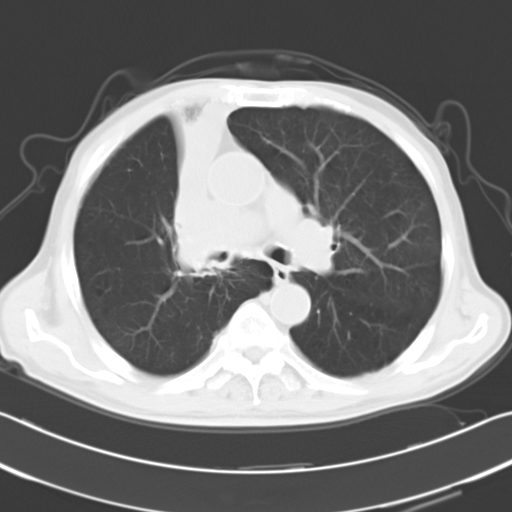
Chest CT, one axial slice. Position 20 of 31 along the scan axis. Reconstruction kernel B40f. Lung window (W 1500 / L -600 HU). 10 mm slice thickness. 512 × 512 image matrix, field of view 339 × 339 mm. Male patient, age 73 years. Case-level facts recorded for this patient, not image findings: clinical TNM (as recorded): T2a N1 M0.
Annotated regions visible in this slice (rectangle marked by the reading radiologist):
- lung tumour (recorded histology: squamous cell carcinoma): box from (x=168, y=91) to (x=229, y=265) px